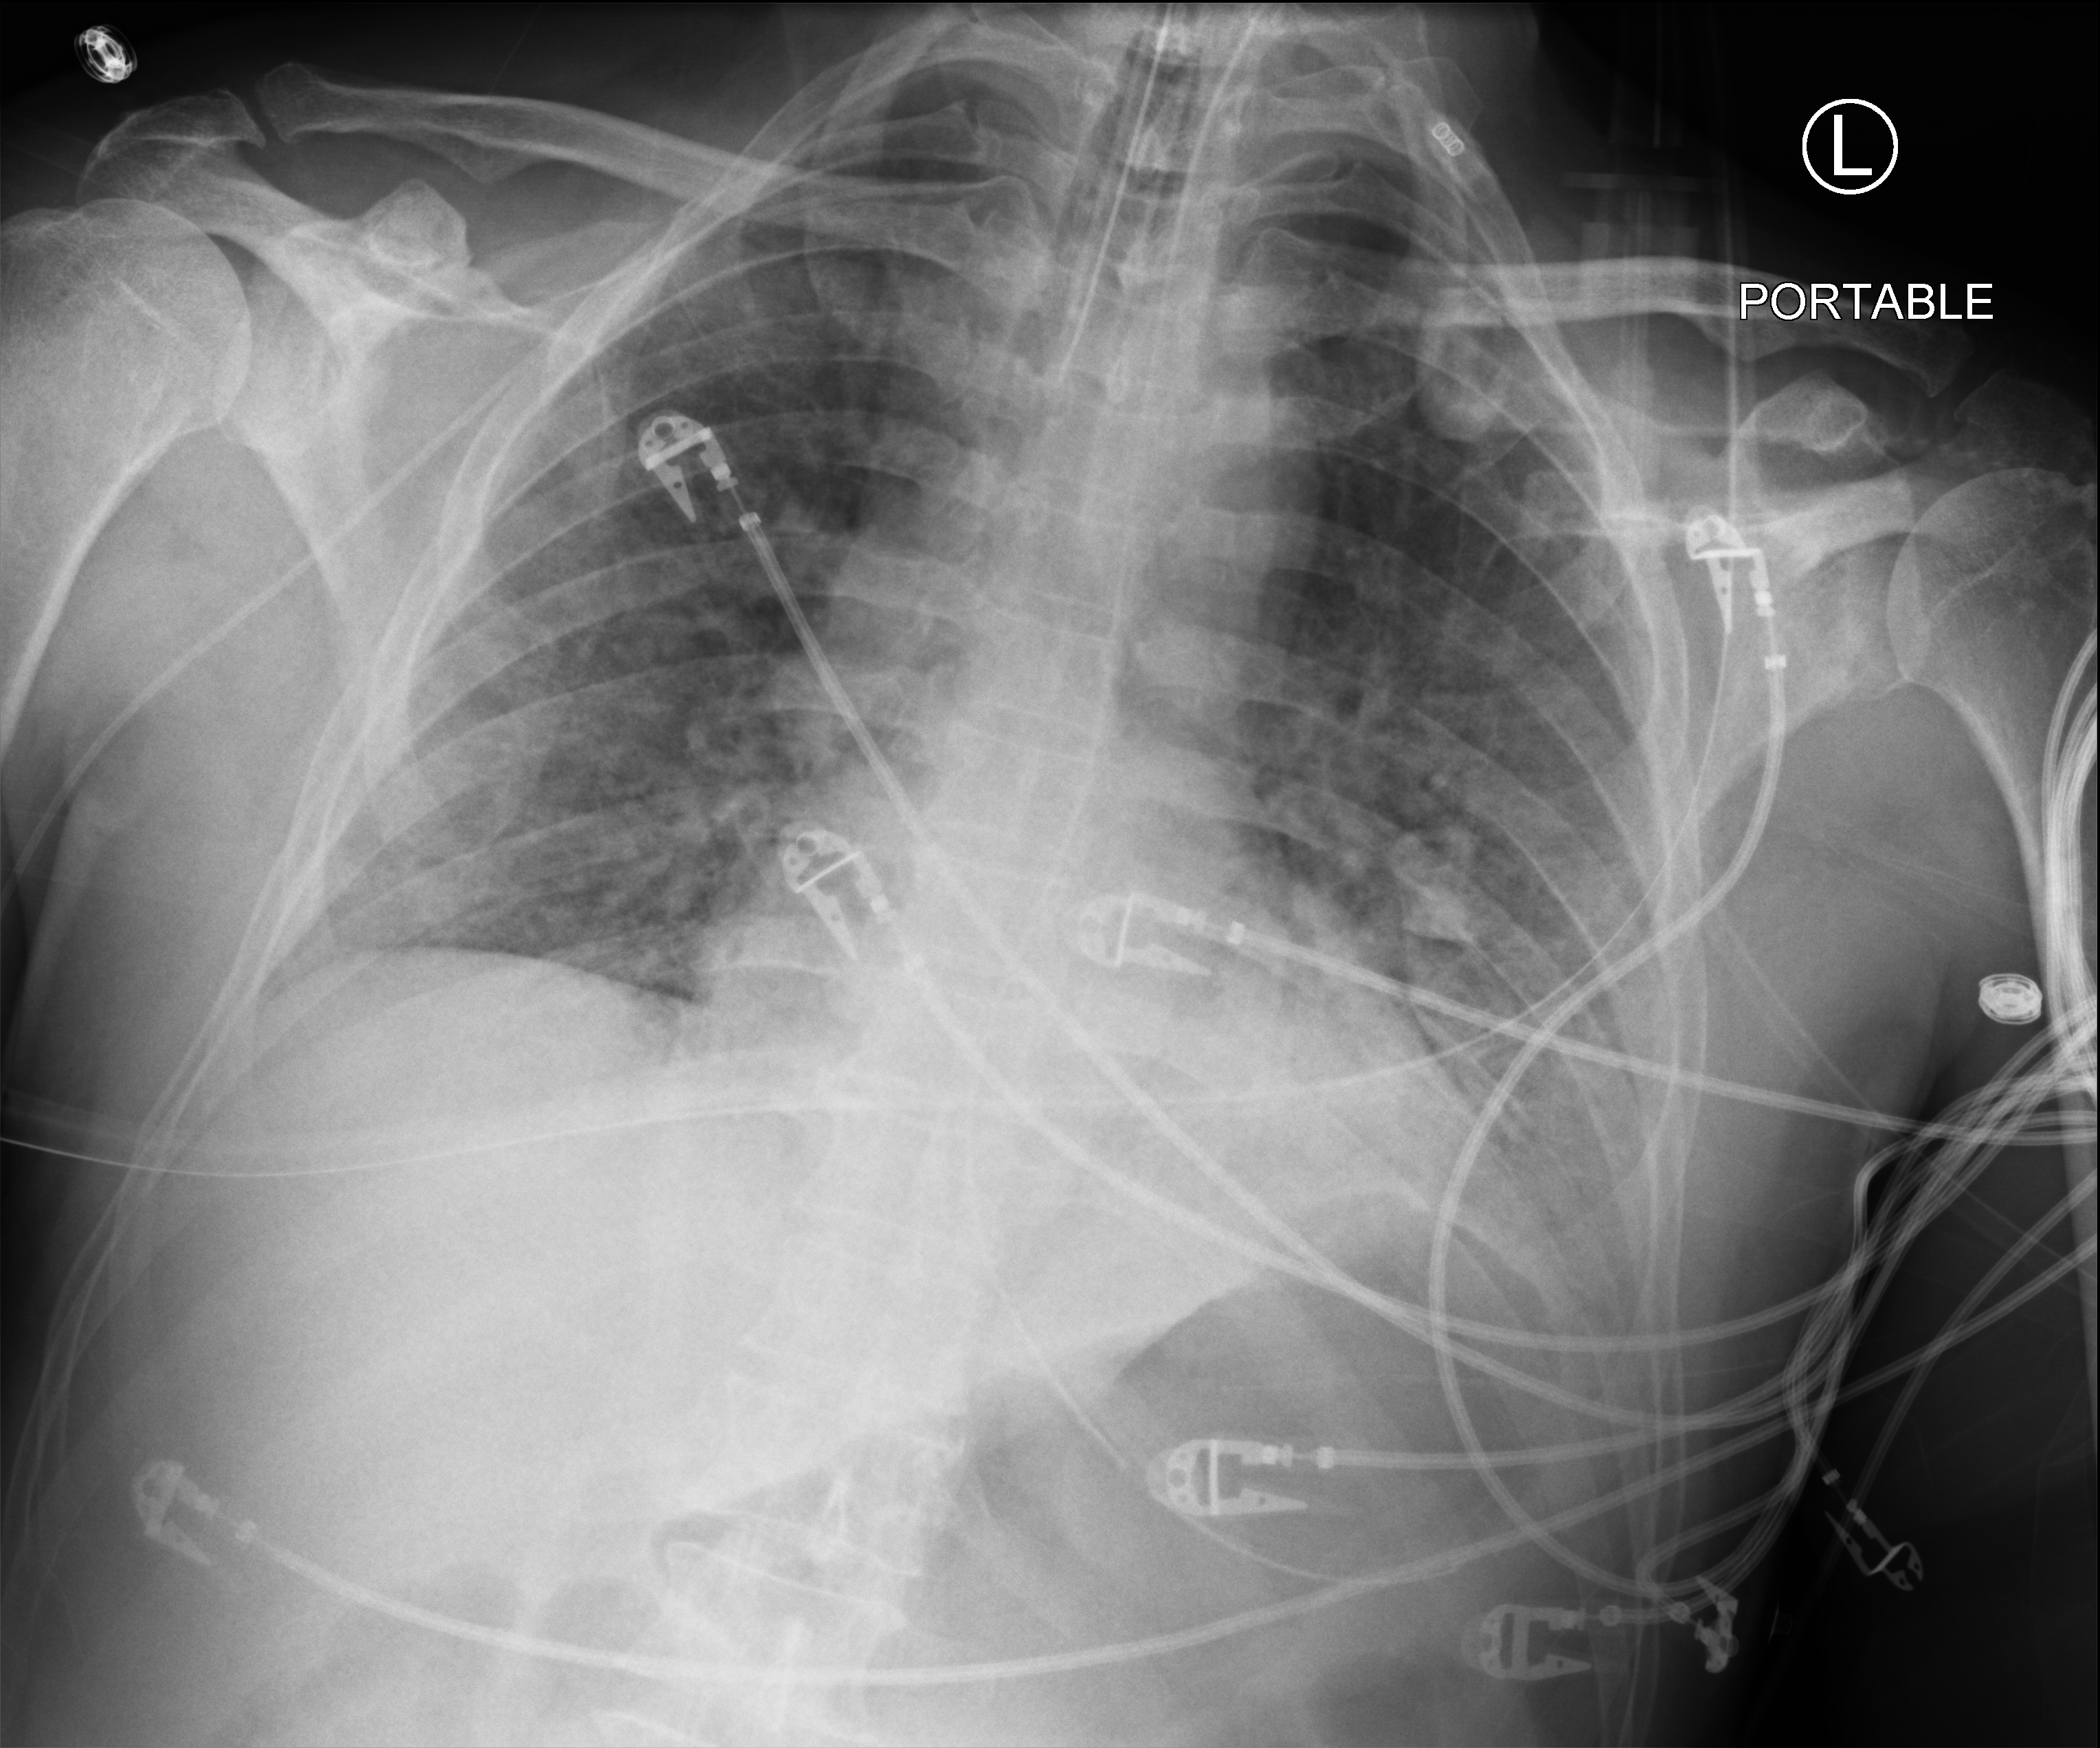
Portable chest radiograph; anteroposterior (AP) projection. Male patient hospitalised with COVID-19, age 60–74 years.
Hospital-stay facts (about this admission, not read from this image; timing relative to this image not recorded): admitted to intensive care during this hospital stay: yes; mechanically ventilated during this hospital stay: yes; hypertension (admission record): yes.